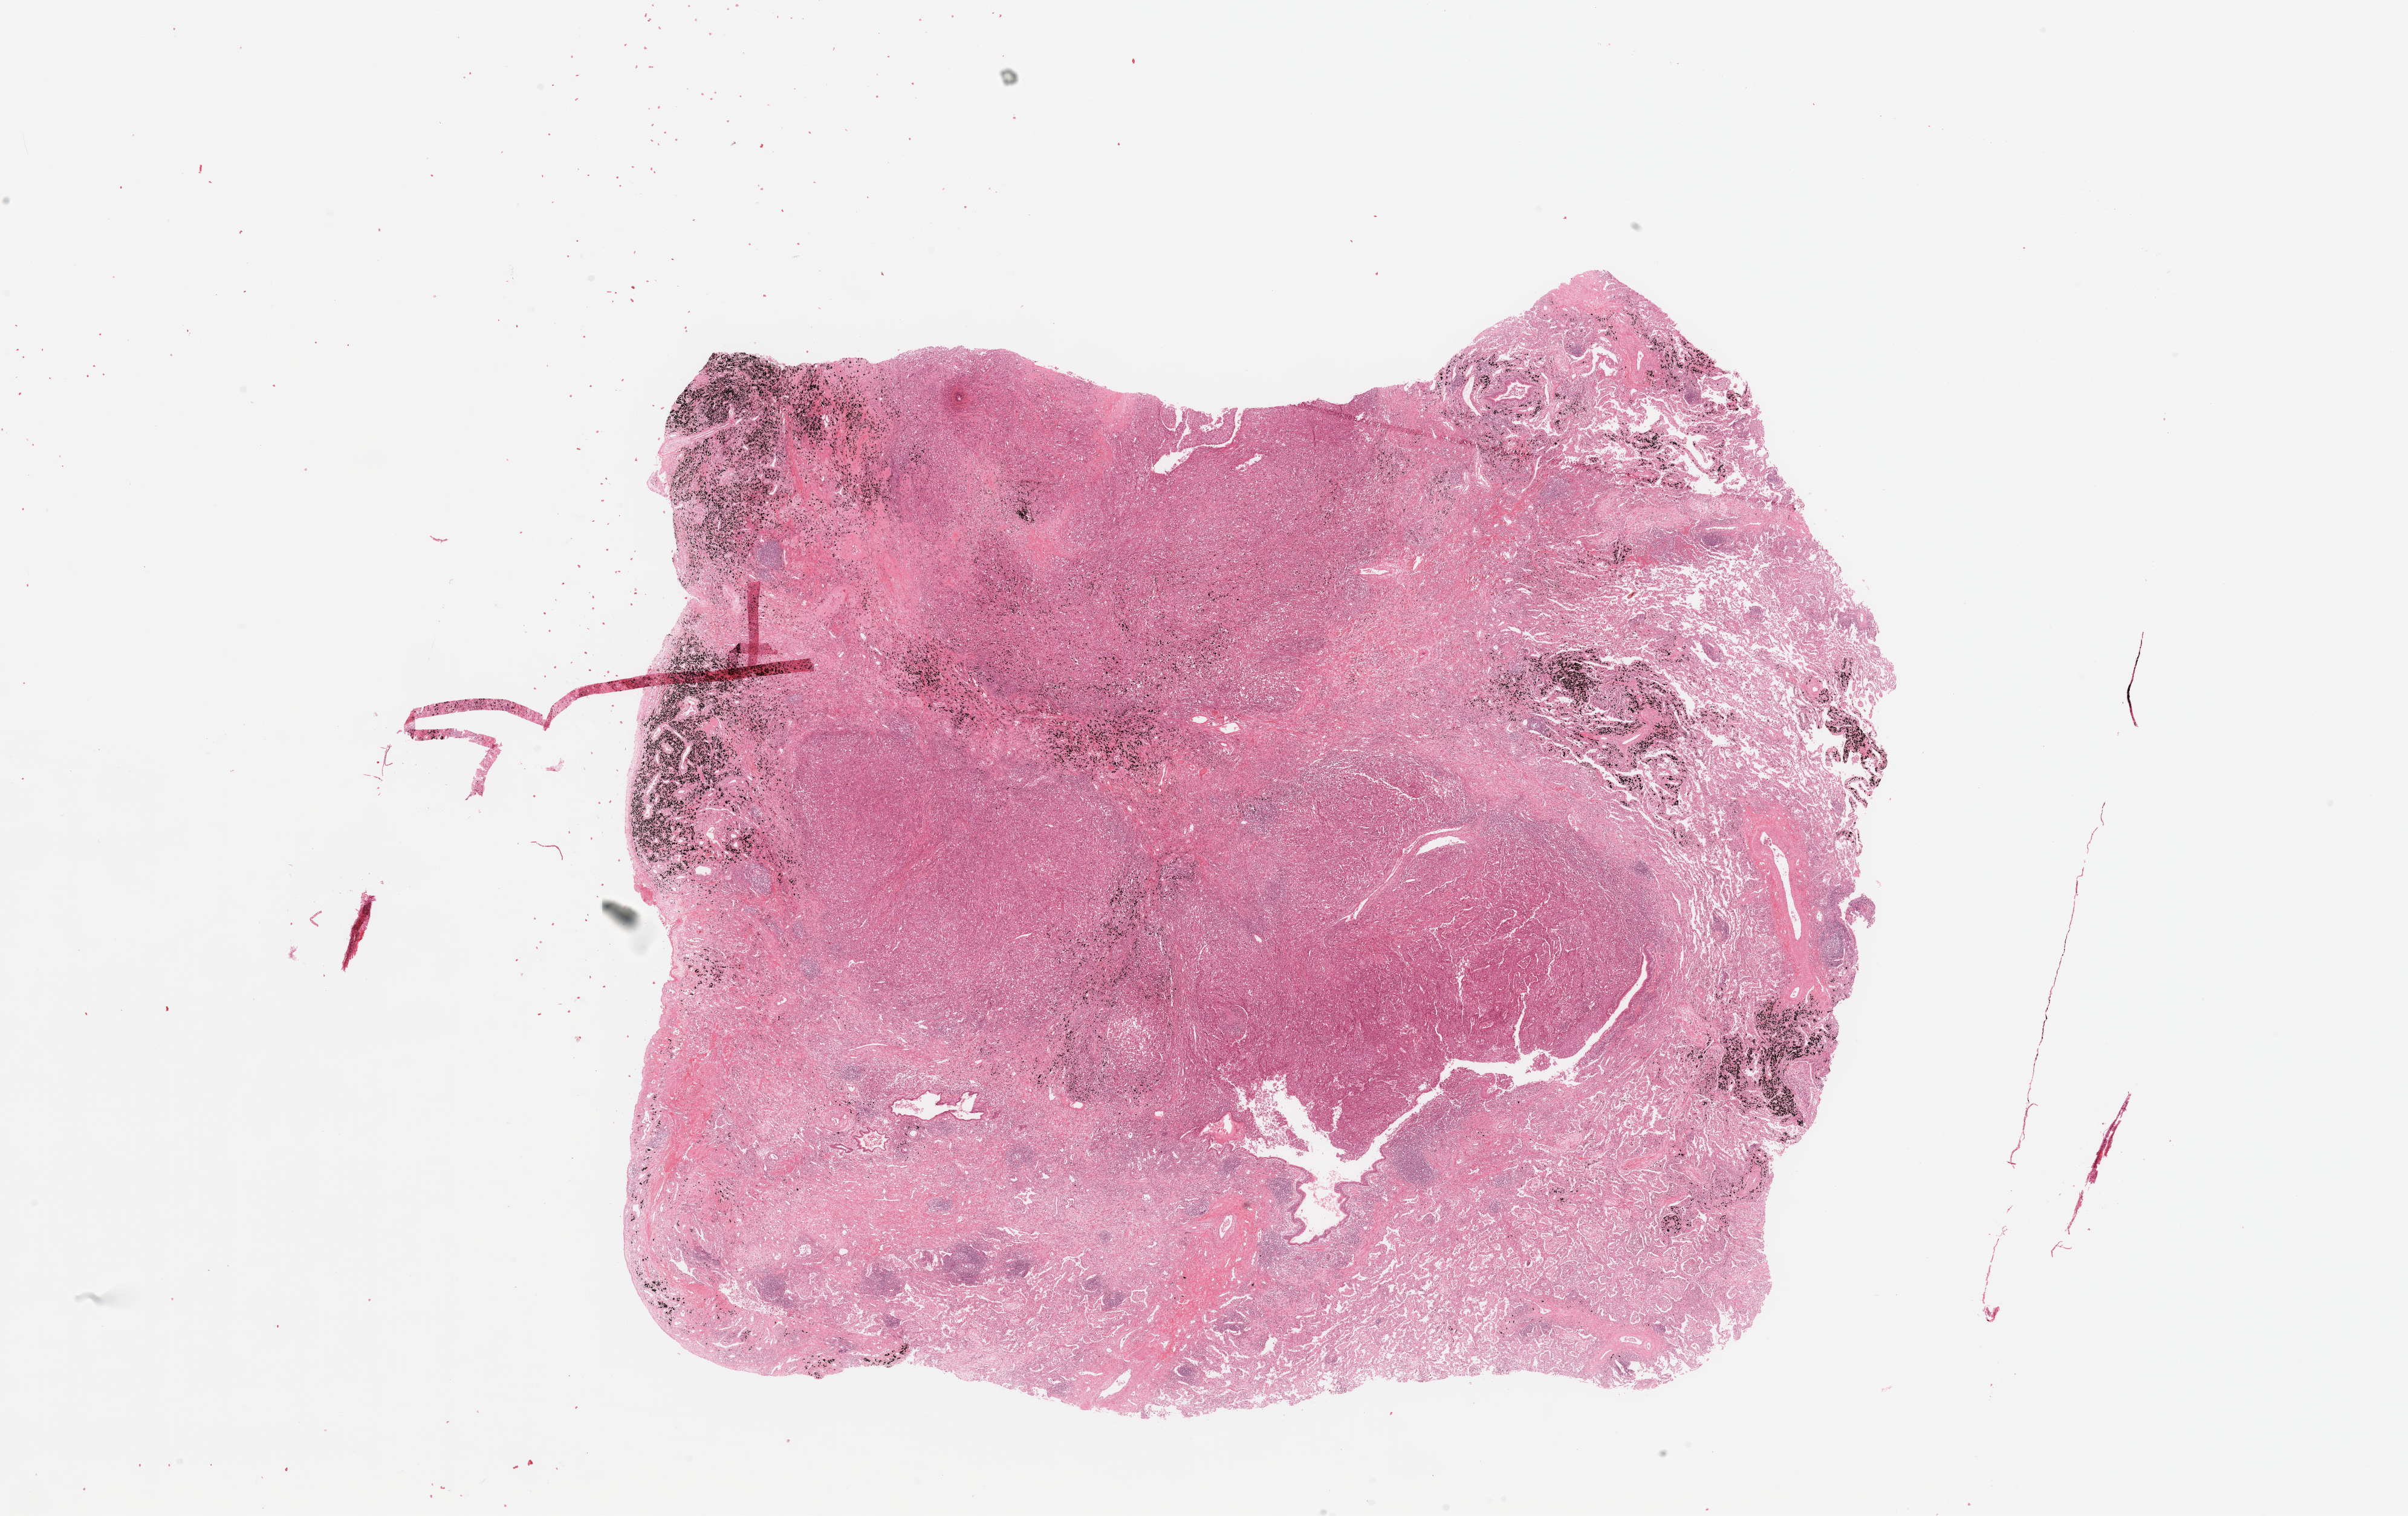
Whole-slide histology image, H&E-stained, shown as a low-resolution overview of the whole scanned area (about 31.5 x 19.8 mm). Tumour tissue sample, lung. Male, 54 y/o. Histologic grade: G3 (poorly differentiated).
Diagnosis: Adenocarcinoma, NOS. AJCC pathologic stage: IIIA.